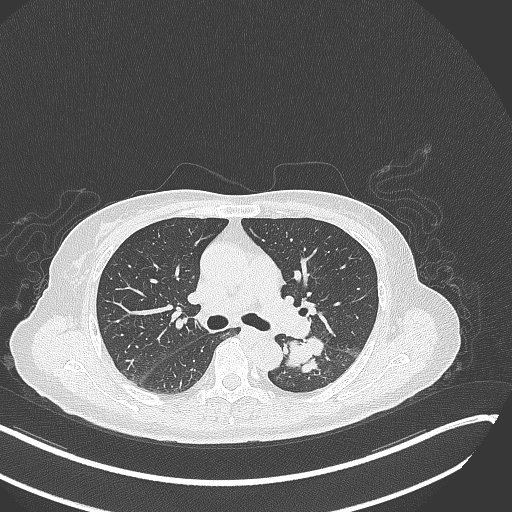
Chest CT, one axial slice; position 174 of 342 along the scan axis; reconstruction kernel B70f; 120 kVp; lung window (W 1500 / L -600 HU); 1 mm slice thickness; 512 × 512 image matrix, field of view 400 × 400 mm. Female patient, age 64 years. From the clinical record (not read from this slice): clinical TNM (as recorded): T3 N1 M1.
Annotated regions visible in this slice (bounding box drawn by a radiologist):
- lung tumour (recorded histology: small cell carcinoma): bounding box (x1, y1, x2, y2) in pixels: (281, 333, 326, 378)